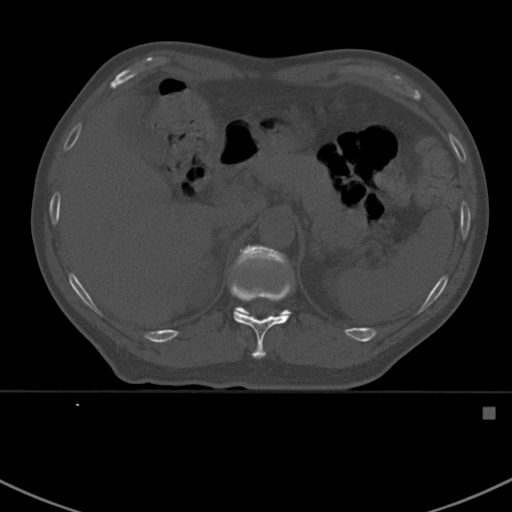
CT including the spine, one axial slice. 120 kVp. Bone window (W 1800 / L 400 HU). 512 × 512 image matrix. Patient: male, 59 years. Case-level facts recorded for this patient, not image findings: primary cancer: prostate.
Annotated regions visible in this slice (semi-automatically segmented with operator editing):
- T11 vertebra: bounding box [x1, y1, x2, y2] px = [230, 279, 293, 359]
- T12 vertebra: [230, 245, 290, 315]